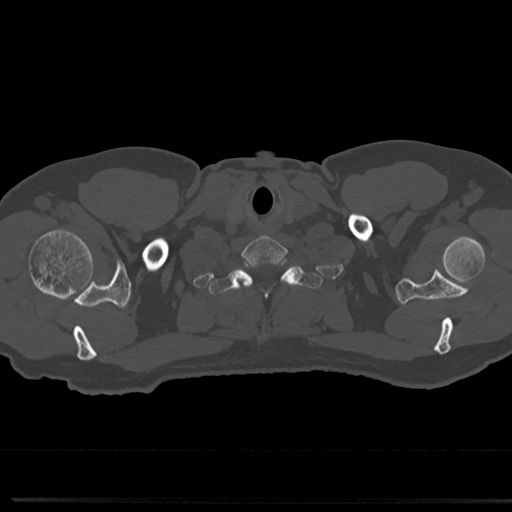
CT including the spine, one axial slice. Position 687 of 817 along the scan axis. Reconstruction kernel Br40s/3. Bone window (W 1800 / L 400 HU). 0.5 mm slice thickness. 512 × 512 image matrix. Male patient, age 61 years. Case-level facts recorded for this patient, not image findings: primary cancer: prostate.
Outlined on this slice (semi-automatically segmented with operator editing):
- T1 vertebra: box from (x=212, y=261) to (x=317, y=344) px